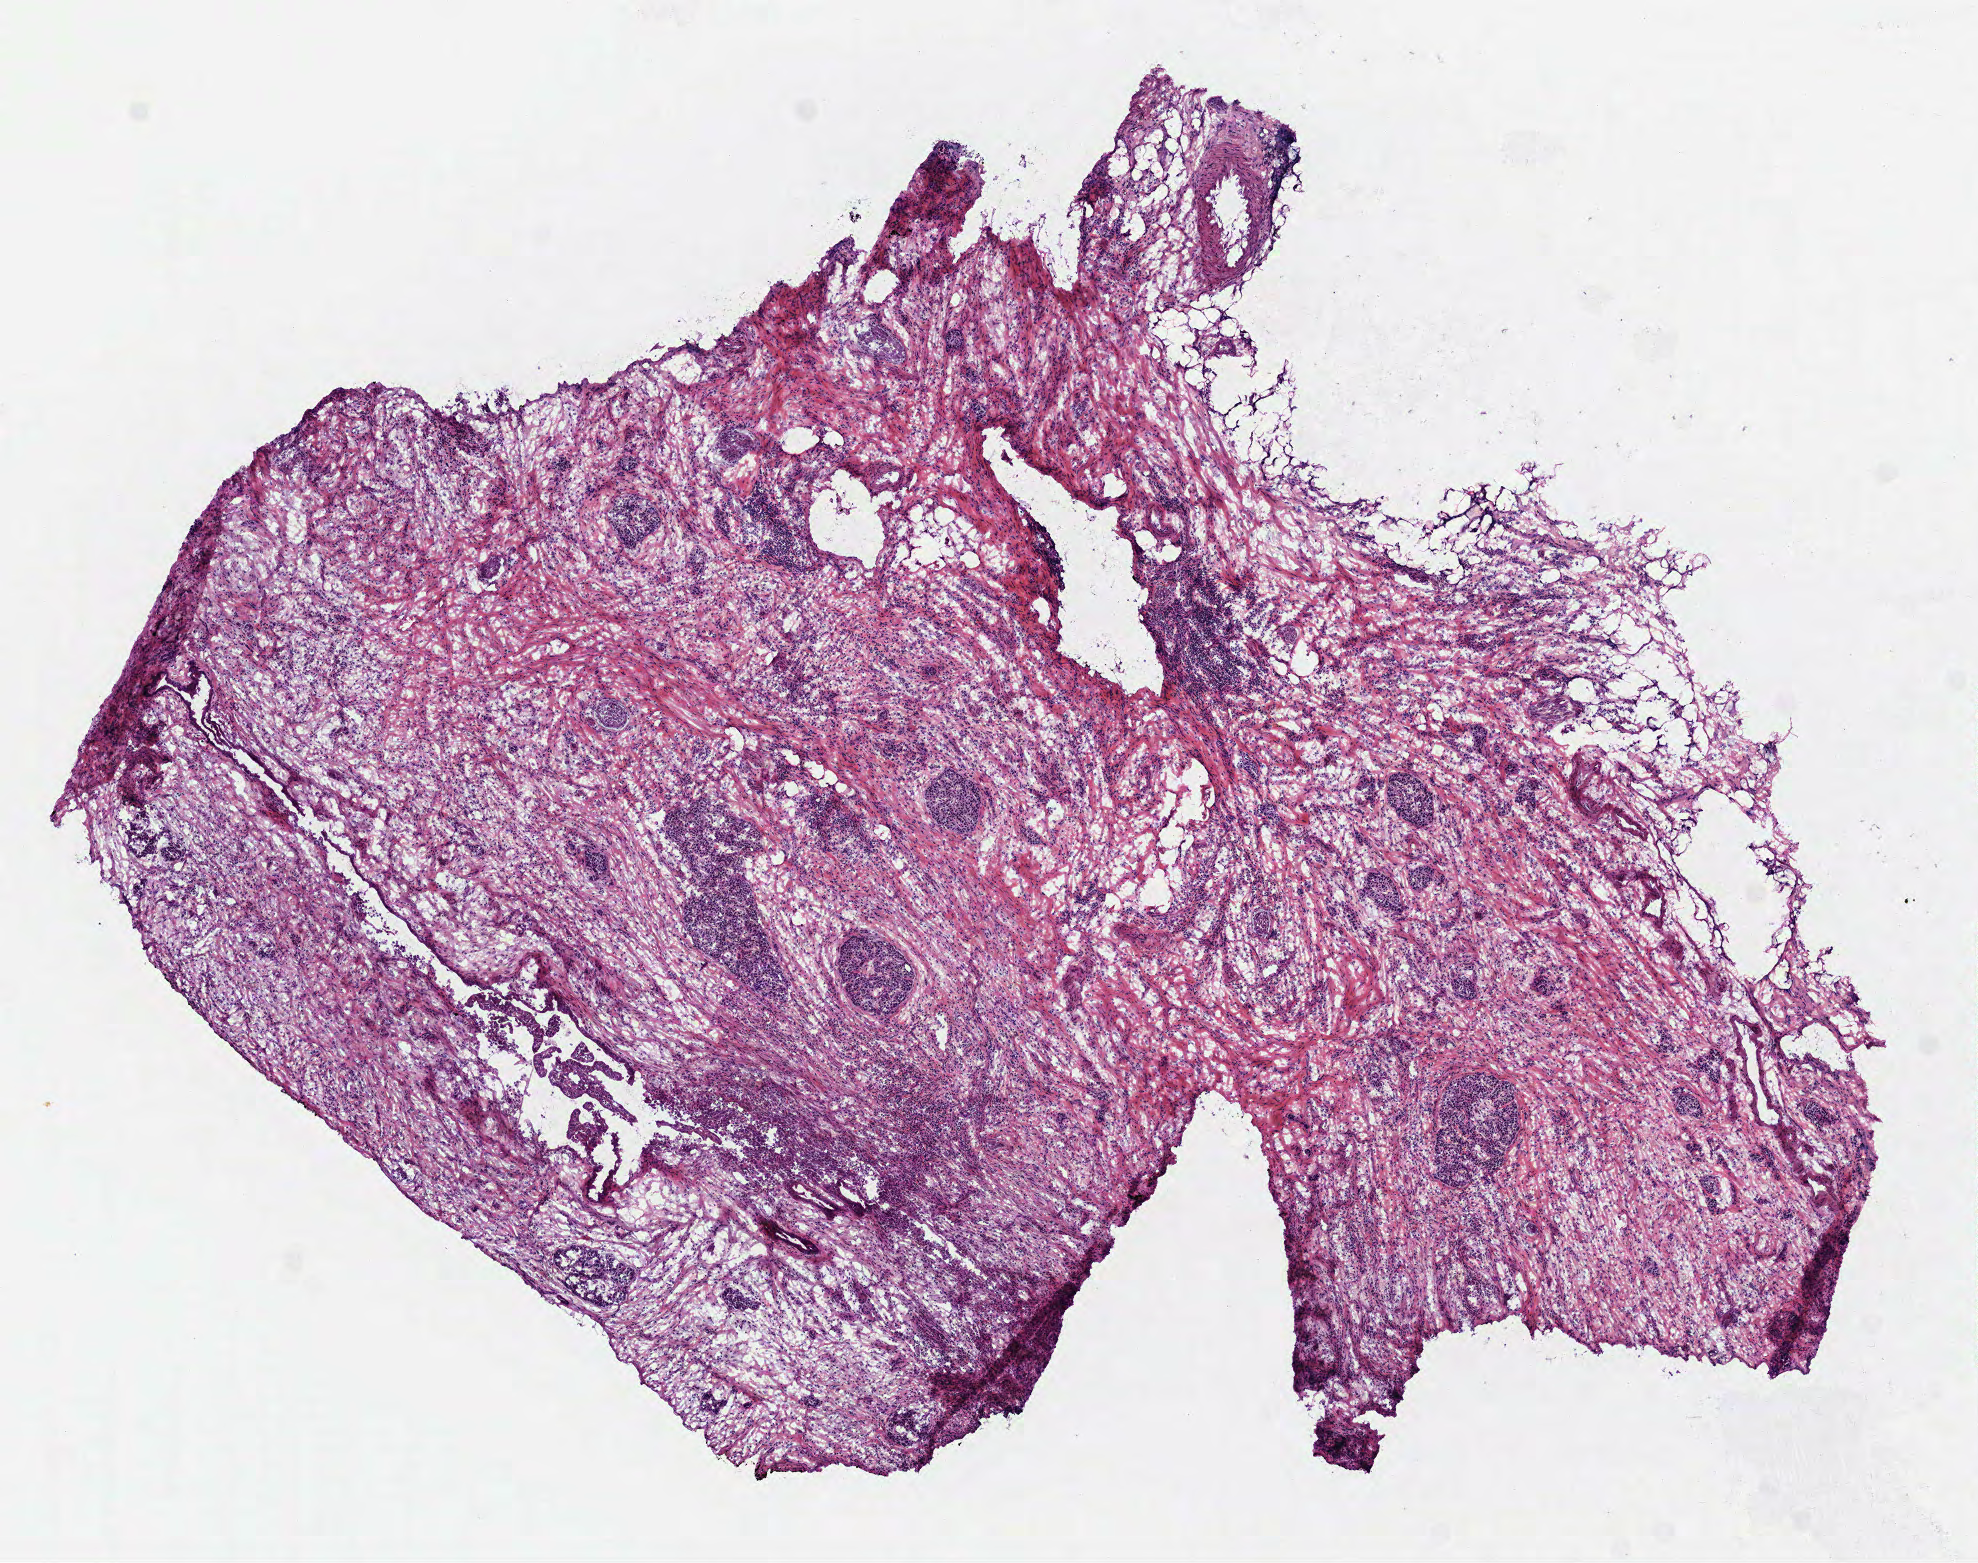
H&E whole-slide image — whole scanned area (about 8.0 x 6.3 mm, slide scanned at 40x) shown as a low-resolution overview. Frozen section from the top of the tissue portion. Sample: primary tumour, pancreas. Male patient; age at initial diagnosis 71 years. Histologic grade: G2 (moderately differentiated). Composition of this section per pathologist review: tumour cells 30%, tumour nuclei 50%, normal cells 0%, stromal cells 70%, necrosis 0%.
• histologic diagnosis: Infiltrating duct carcinoma, NOS (head of pancreas)
• AJCC pathologic stage: IB (7th edition)
• TNM: T2 N0 MX